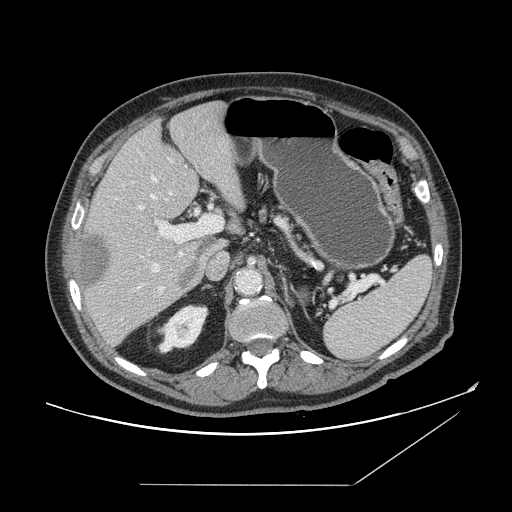
Contrast-enhanced abdominal CT, one axial slice. Position 98 of 166 along the scan axis. 120 kVp. Intravenous contrast given. Soft-tissue window (W 400 / L 40 HU). 2.5 mm slice thickness. 512 × 512 image matrix, field of view 416 × 416 mm. Male patient, age 80 years. From the clinical record (not read from this slice): diagnosis: colorectal cancer liver metastases, imaged before liver resection; multiple liver metastases: no; largest metastasis: 2.2 cm; chemotherapy before resection: no.
Outlined on this slice (outlined manually by an expert reader):
- hepatic veins: bounding box (x1, y1, x2, y2) in pixels: (138, 177, 173, 289)
- liver: (78, 102, 247, 346)
- planned liver remnant (the part of the liver to remain after resection): (92, 102, 245, 256)
- portal vein (with intrahepatic branches): (140, 206, 223, 293)
- liver metastasis: (82, 235, 200, 290)